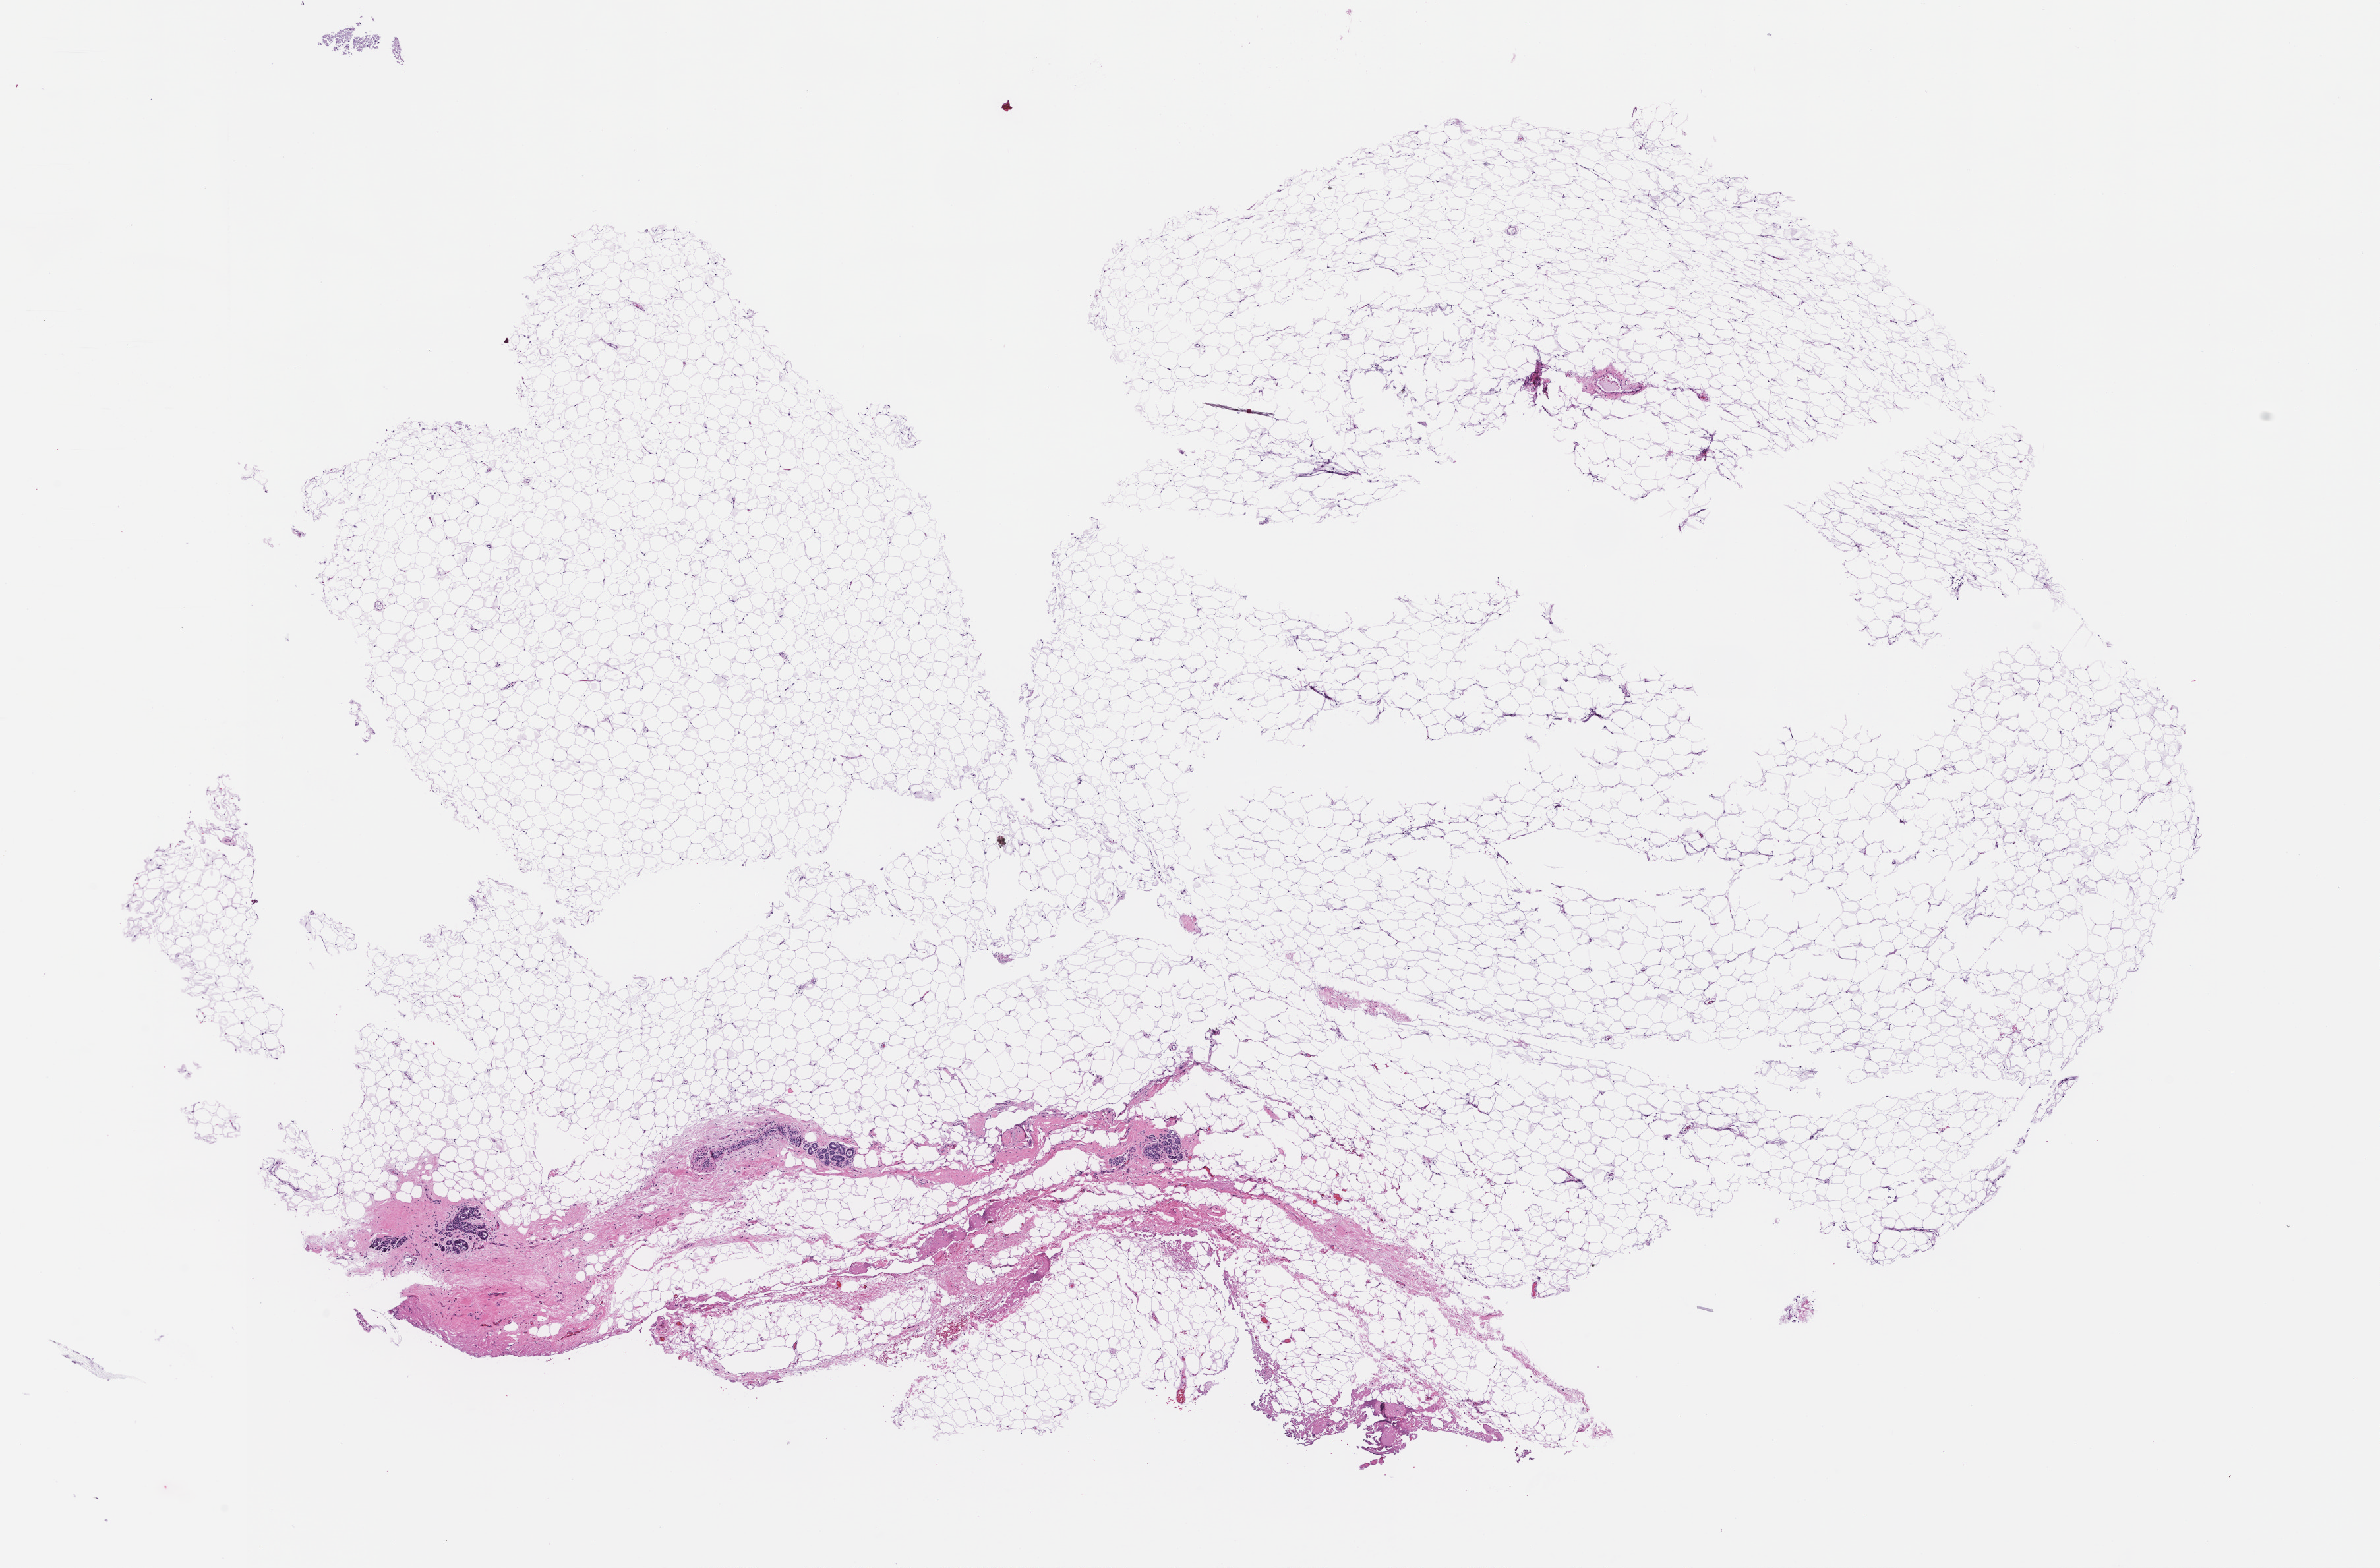
Whole-slide image, hematoxylin and eosin (H&E) stain, a low-resolution overview of the entire scanned area, about 14.6 x 9.6 mm. FFPE section. Site: breast. Specimen time point: collected post-treatment, no progression. Patient sex: female.
This section: primary tumour tissue. Diagnosis: Invasive Breast Carcinoma.